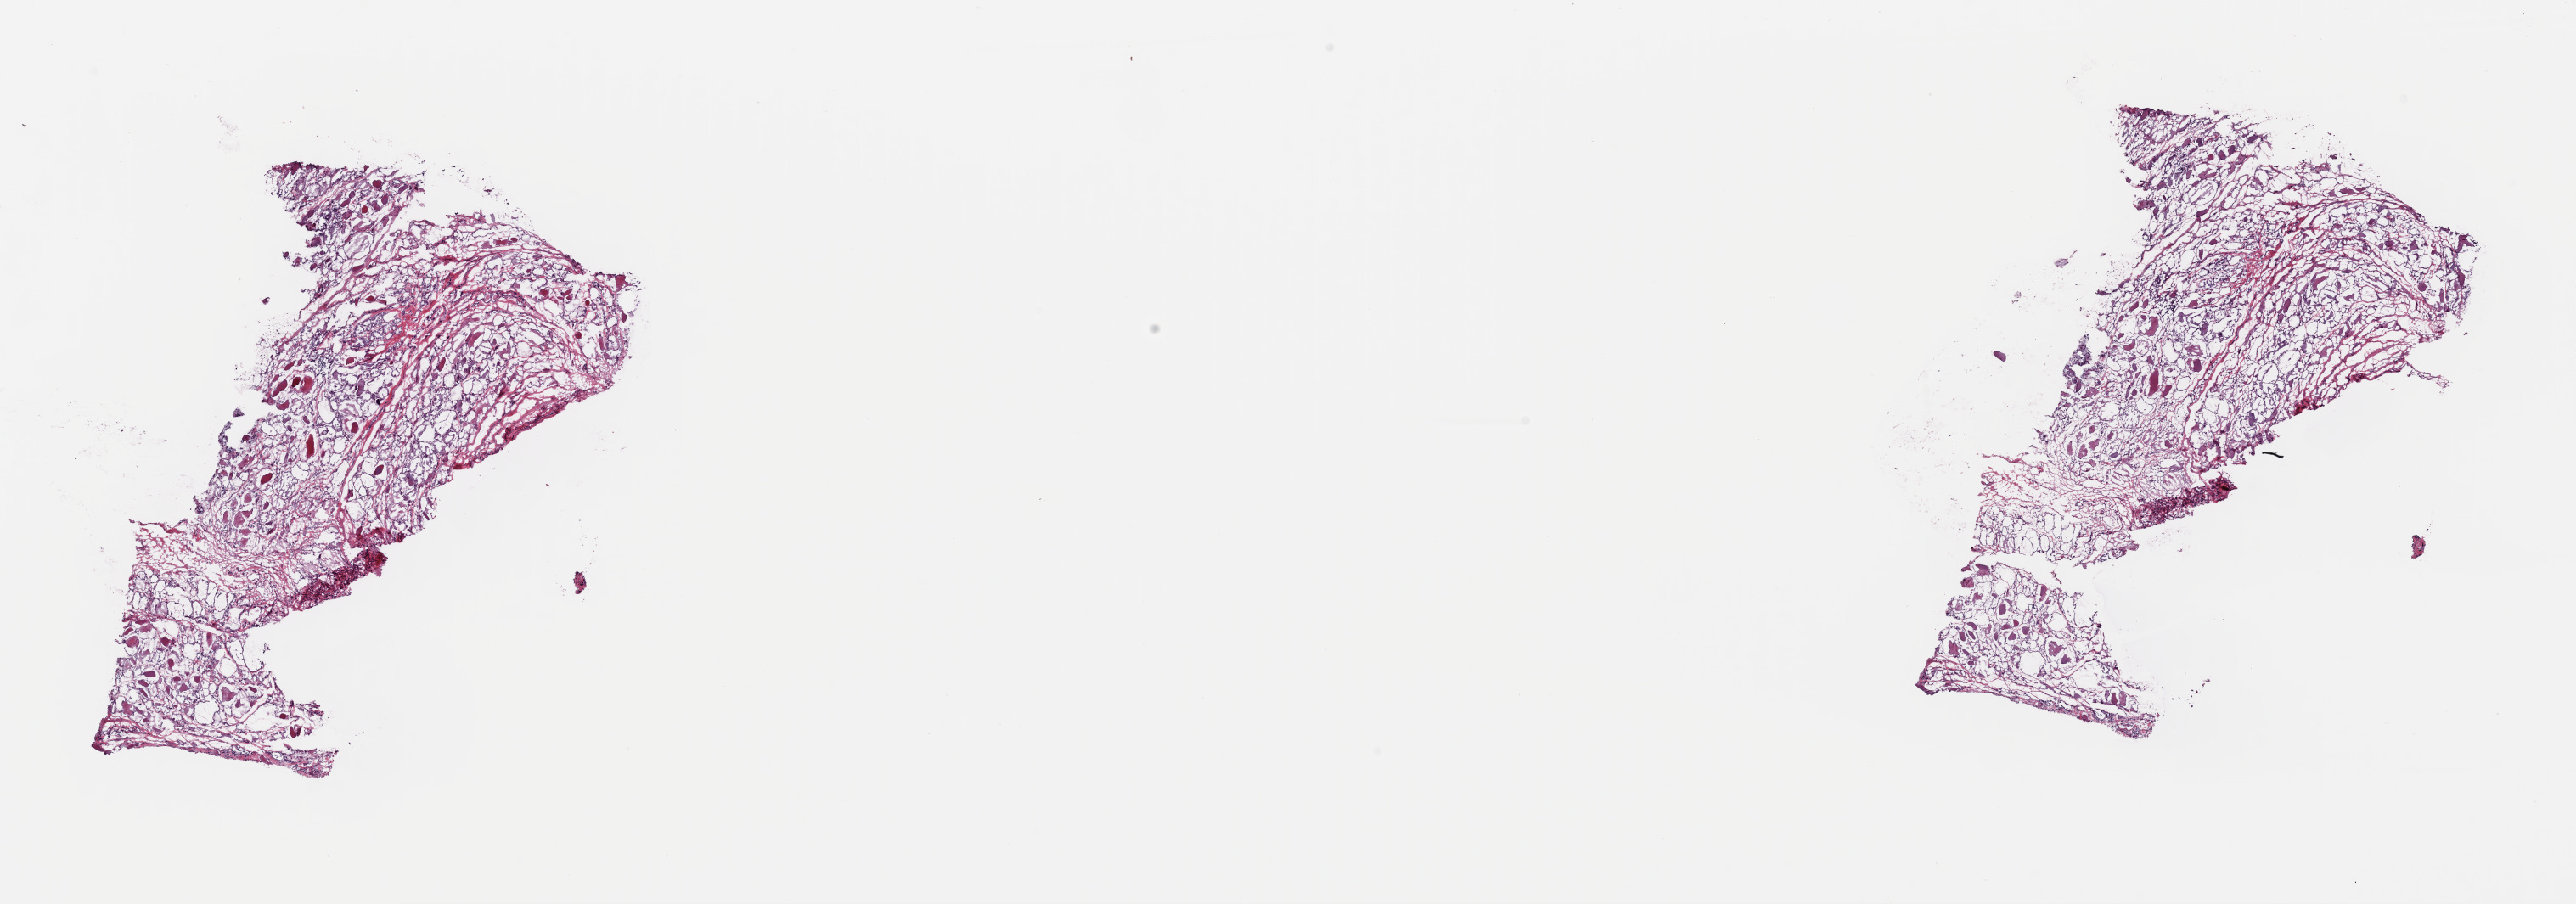
Hematoxylin and eosin (H&E) stained whole-slide image, a low-resolution overview of the entire scanned area, about 24.0 x 8.4 mm. Frozen section from the top of the tissue portion. Primary tumour sample from the thyroid. Male patient. Slide review estimates, as recorded: tumour cells 100%, tumour nuclei 90%, normal cells 0%, stromal cells 0%, necrosis 0%. Inflammatory infiltration, as recorded: lymphocyte infiltration 0%, monocyte infiltration 0%, neutrophil infiltration 0%.
• laterality: bilateral
• diagnosis: Papillary adenocarcinoma, NOS (thyroid gland)
• lymph nodes positive (case pathology): 10 of 41 examined
• AJCC pathologic stage: III (5th edition)